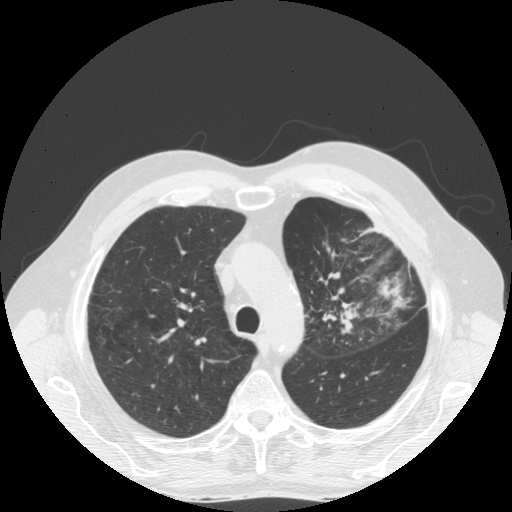
Low-dose screening chest CT, one axial slice; position 129 of 170 along the scan axis; lung window (W 1500 / L -600 HU); 512 × 512 image matrix.
Outlined on this slice (expert manual segmentation):
- lesion 1 (tumor, upper lobe of left lung): bounding box [x1, y1, x2, y2] px = [341, 303, 361, 334]